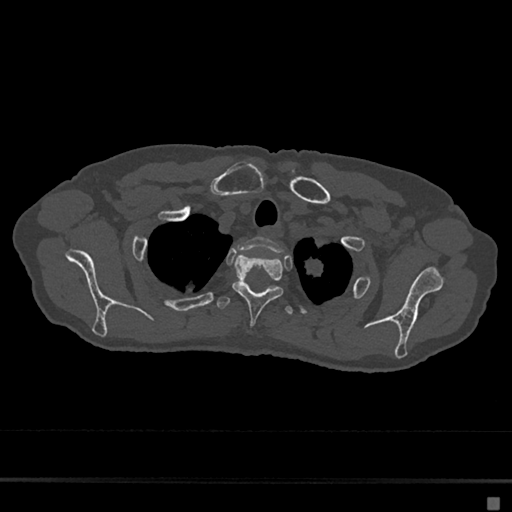
CT including the spine, one axial slice. Reconstruction kernel Br40s/3. 120 kVp. Bone window (W 1800 / L 400 HU). 0.5 mm slice thickness. 512 × 512 image matrix, field of view 360 × 360 mm. Patient: female, 68 years. Case-level facts recorded for this patient, not image findings: primary cancer: renal.
Outlined on this slice (semi-automatic segmentation, software-assisted and operator-edited):
- T1 vertebra: bounding box (x1, y1, x2, y2) in pixels: (238, 237, 283, 253)
- T2 vertebra: (232, 254, 284, 324)
- T3 vertebra: (216, 296, 293, 315)